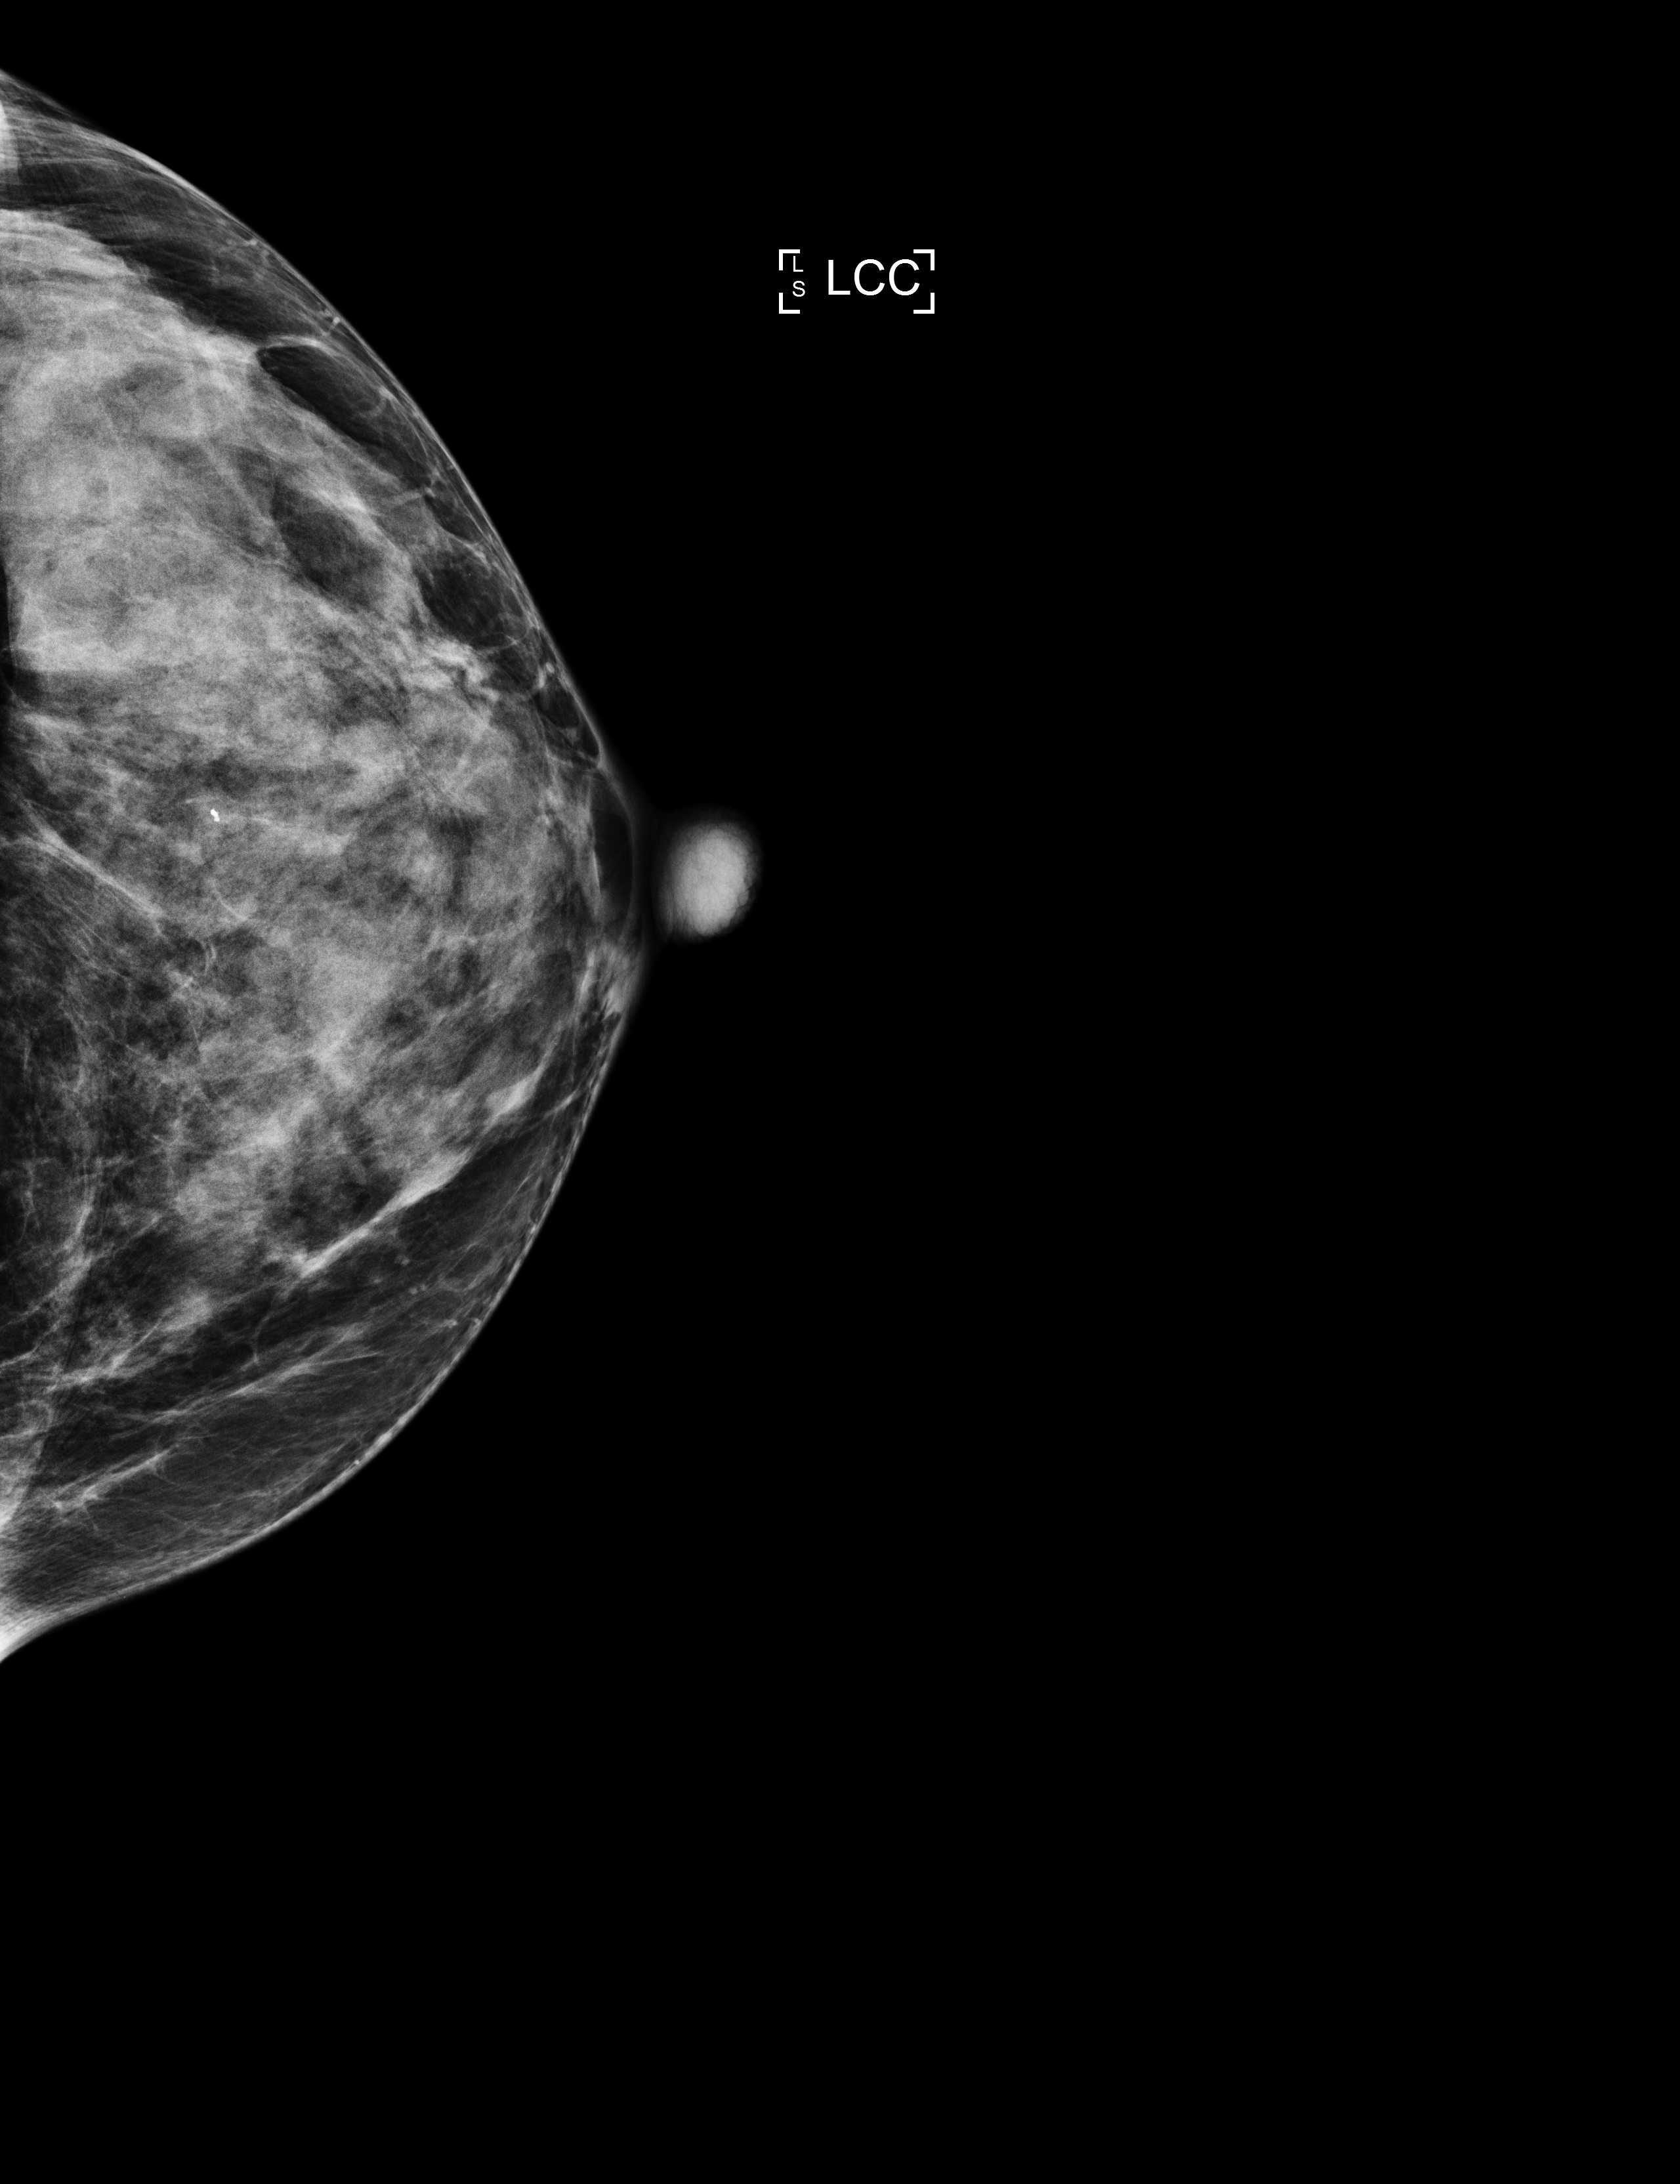
Annual screening mammography examination. Female patient, age 68 years.
Image type: full-field digital mammogram. Breast: left. Projection: CC view.